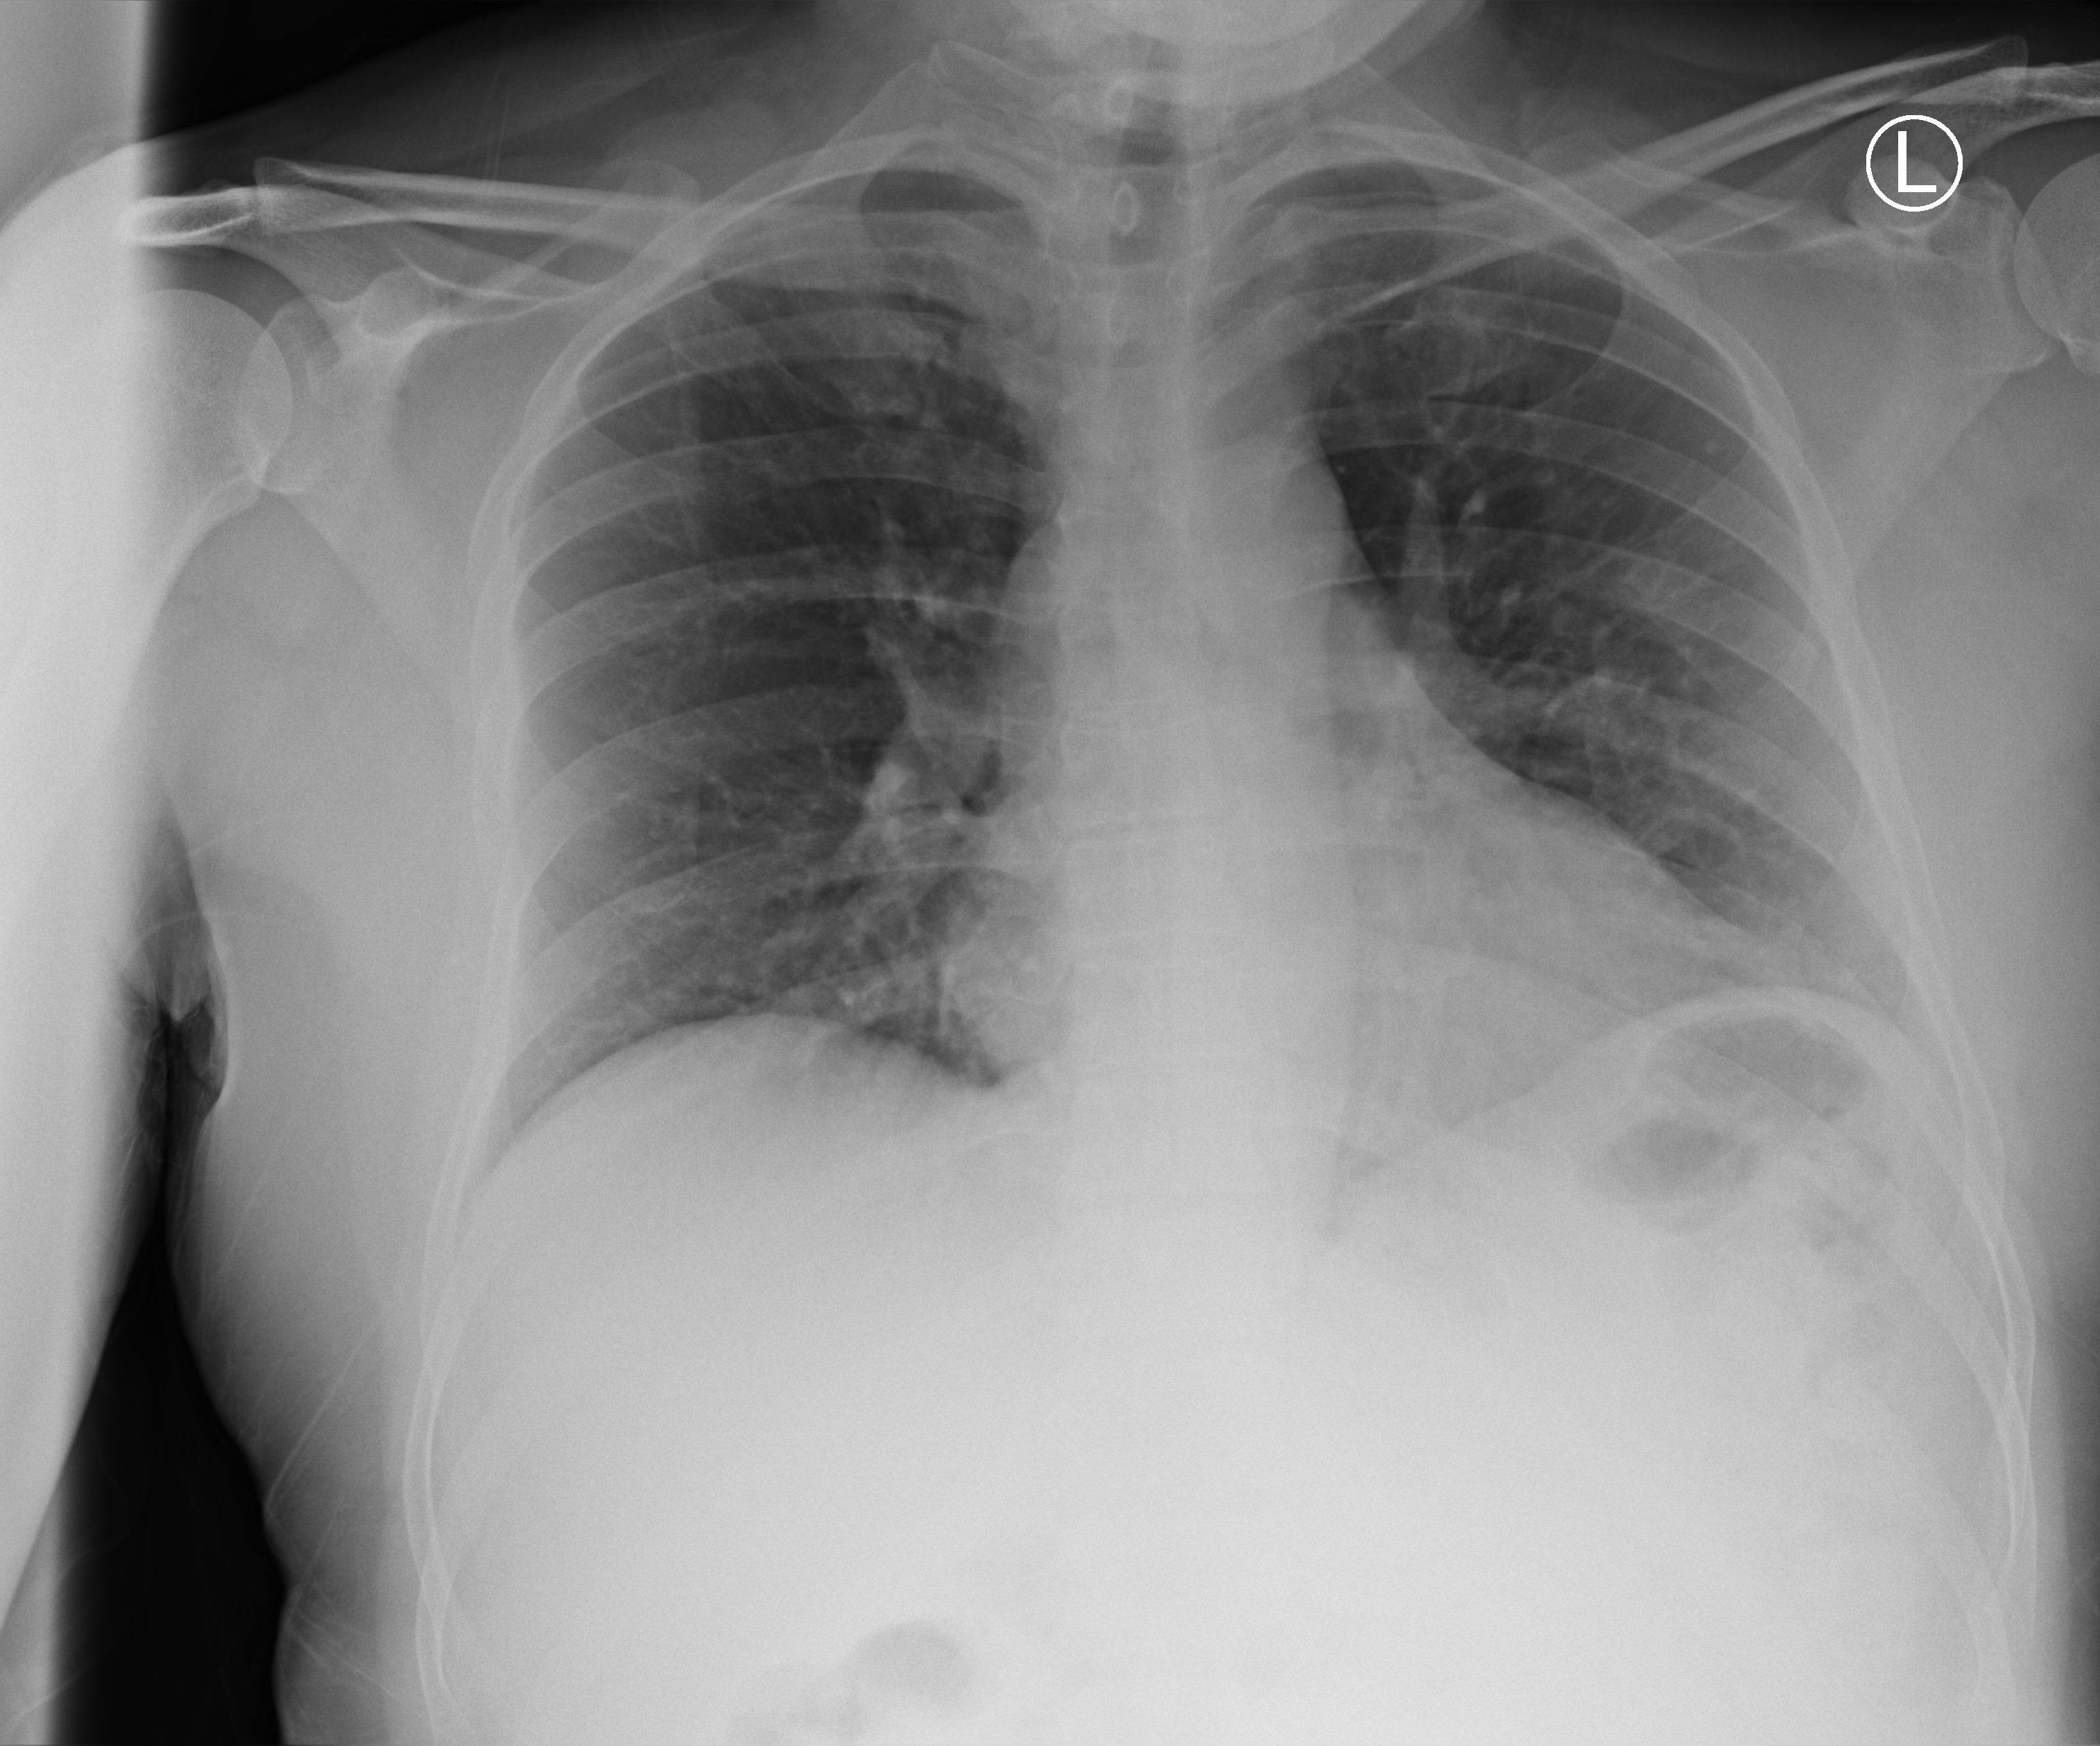
Chest X-ray (portable). Patient hospitalised with COVID-19; male, aged 18–59 years.
Hospital-stay facts (about this admission, not read from this image; timing relative to this image not recorded): other chronic lung disease (admission record): no; diabetes (admission record): no.